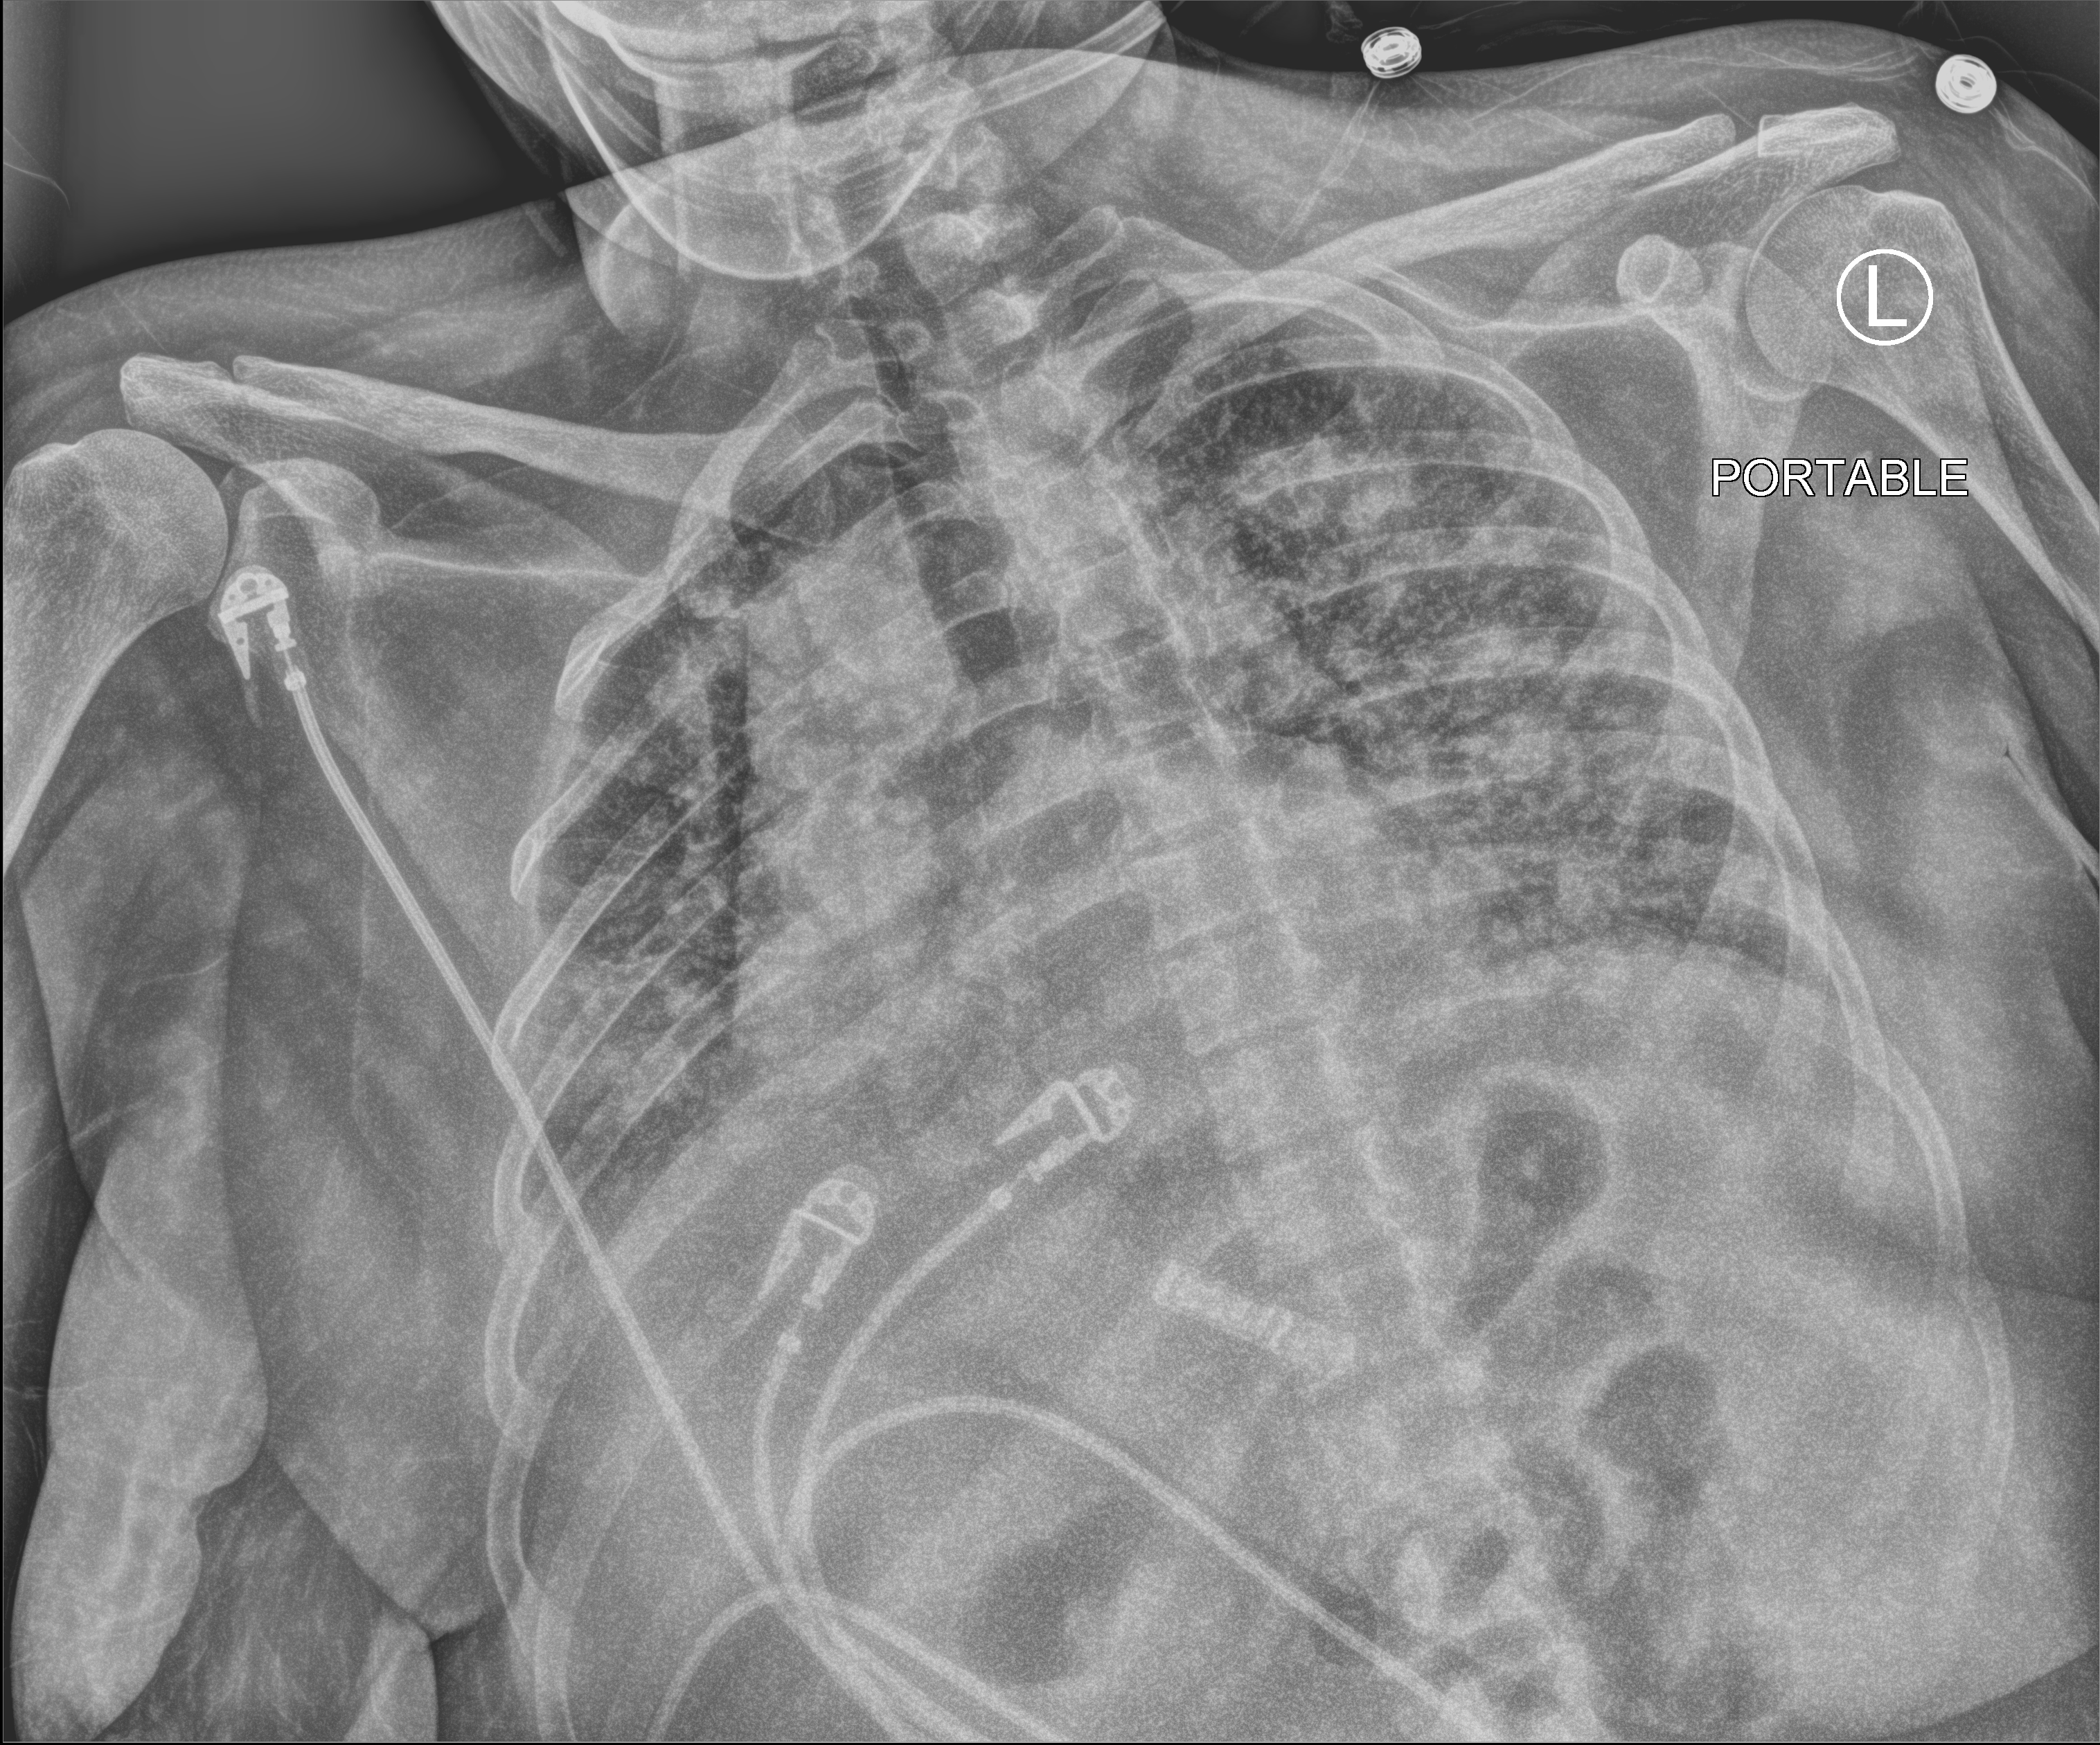
Portable chest radiograph. Patient hospitalised with COVID-19; female, aged 18–59 years.
Admission-level facts for this patient (not findings on this image; timing relative to this image not recorded):
- admitted to intensive care during this hospital stay: no
- length of hospital stay: 33 days